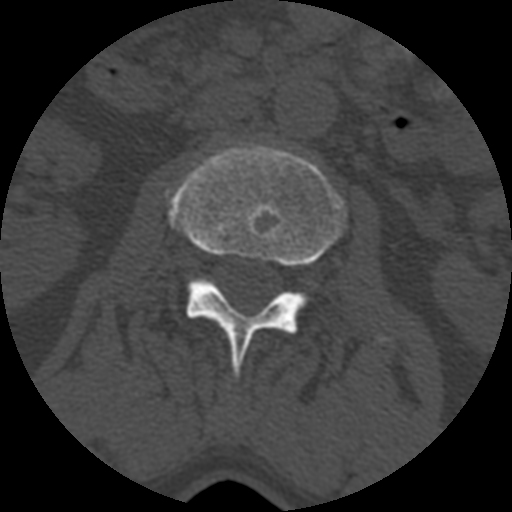
CT including the spine, one axial slice. Position 331 of 399 along the scan axis. Reconstruction kernel STANDARD. 120 kVp. Bone window (W 1800 / L 400 HU). 512 × 512 image matrix, field of view 160 × 160 mm. Patient age 71 years. From the clinical record (not read from this slice): primary cancer: prostate.
Structures marked on this image (semi-automatically segmented with operator editing):
- L2 vertebra: bounding box (x1, y1, x2, y2) in pixels: (168, 144, 394, 379)